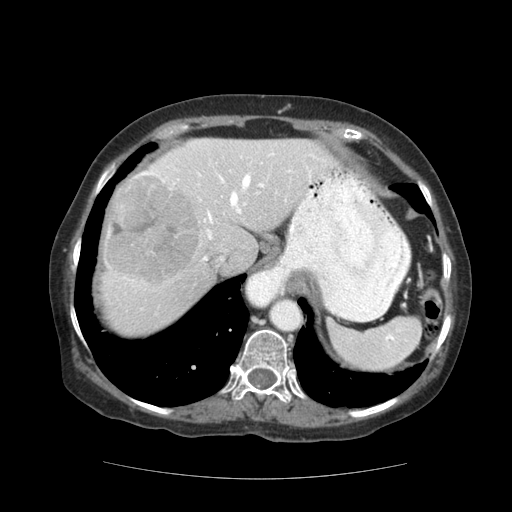
Contrast-enhanced abdominal CT (liver protocol), one axial slice; slice 89 of 111 in the series (ordered by position); 140 kVp; soft-tissue window (W 400 / L 40 HU); 2.5 mm slice thickness; 512 × 512 image matrix, field of view 360 × 360 mm. From the clinical record (not read from this slice): diagnosis: hepatocellular carcinoma (patient treated with transarterial chemoembolisation; whether this scan precedes or follows treatment is not stated here); TNM stage (as recorded): Stage-I; Child-Pugh class: A; tumour differentiation: moderately-poorly differentiated; tumour size: 7.3 cm.
Annotated regions visible in this slice (semi-automatic segmentation, software-assisted and operator-edited):
- abdominal aorta: bounding box [x1, y1, x2, y2] px = [271, 300, 301, 330]
- liver parenchyma outside the tumour (the mass and vessels are separate outlines, so this box may not span the whole liver): [100, 138, 338, 334]
- mass: [104, 177, 201, 286]
- liver vessels: [136, 152, 315, 260]